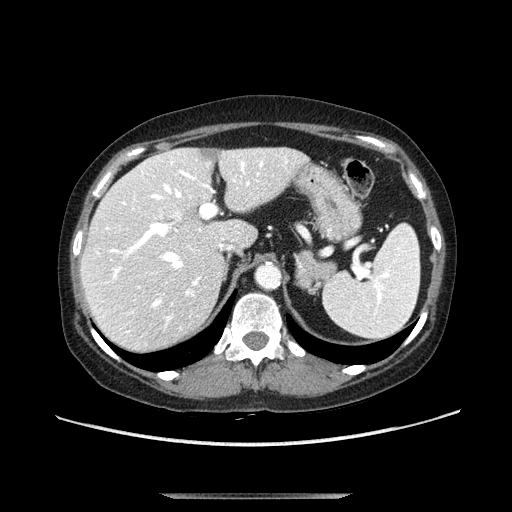
Contrast-enhanced abdominal CT, one axial slice; position 75 of 107 along the scan axis; soft-tissue window (W 400 / L 40 HU); 2.5 mm slice thickness; 512 × 512 image matrix, field of view 380 × 380 mm. Female patient. From the clinical record (not read from this slice): diagnosis: adrenocortical carcinoma; tumour side: left adrenal.
Outlined on this slice (semi-automatic segmentation, software-assisted and operator-edited):
- mass: bounding box (x1, y1, x2, y2) in pixels: (295, 250, 338, 289)